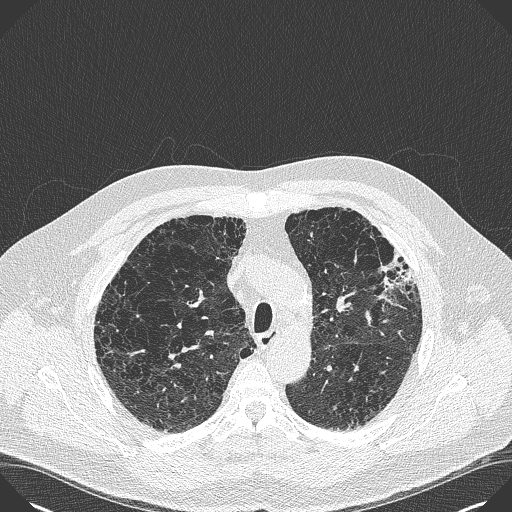
Chest CT (low-dose screening protocol), one axial image. Baseline screening round. Lung window (W 1500 / L -600 HU). 1 mm slice thickness. 512 × 512 image matrix. Male participant, aged 59 years at enrolment. Current smoker at enrolment.
Expert reader's lesion annotation, bounding box [x1, y1, x2, y2] px = [373, 247, 428, 298]. Screening reader's record for this exam: no non-calcified nodule ≥4 mm recorded.